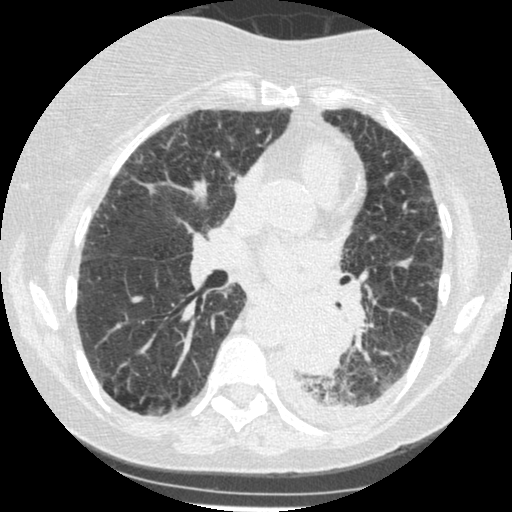
Low-dose screening chest CT, one axial slice. Lung window (W 1500 / L -600 HU). 1.25 mm slice thickness. 512 × 512 image matrix, field of view 310 × 310 mm.
Structures marked on this image (outlined manually by an expert reader):
- lesion 1 (tumor, lower lobe of left lung): bounding box (x1, y1, x2, y2) in pixels: (284, 304, 347, 375)